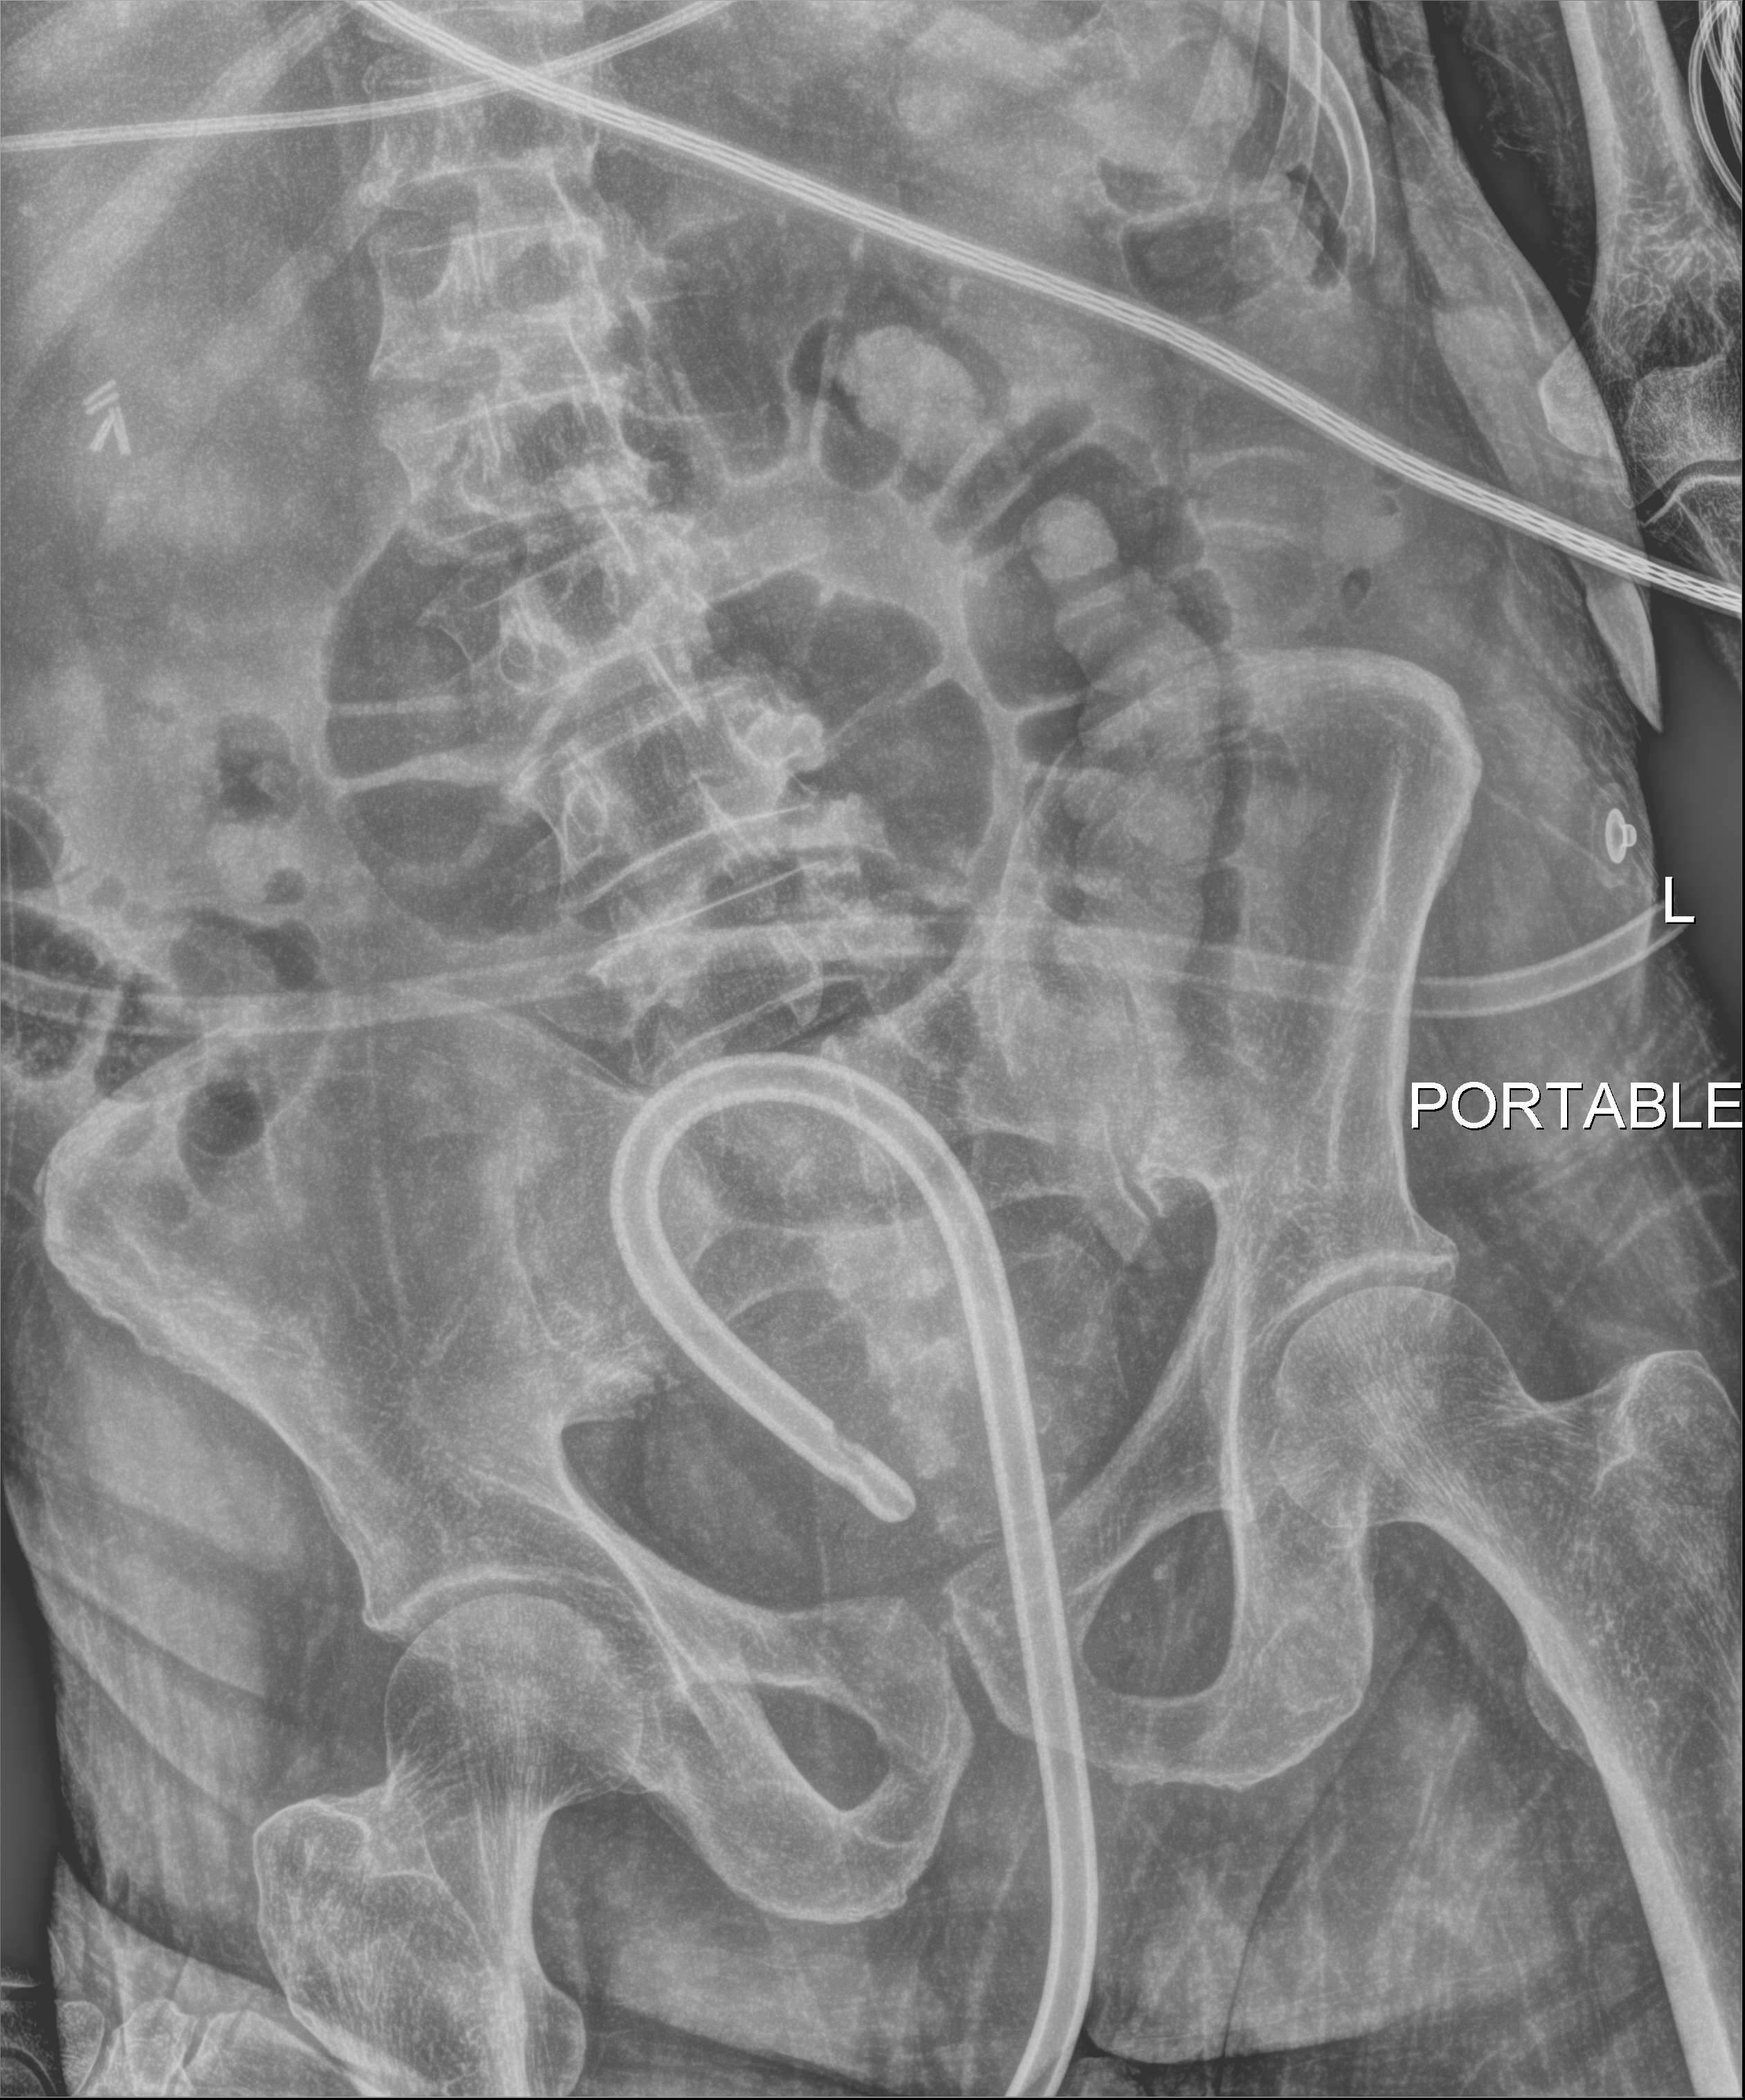
Abdomen radiograph (digital radiography). Patient hospitalised with COVID-19; male, aged 75–90 years.
Admission-level facts for this patient (not findings on this image; timing relative to this image not recorded): hypertension (admission record): no; admitted to intensive care during this hospital stay: yes; mechanically ventilated during this hospital stay: yes.